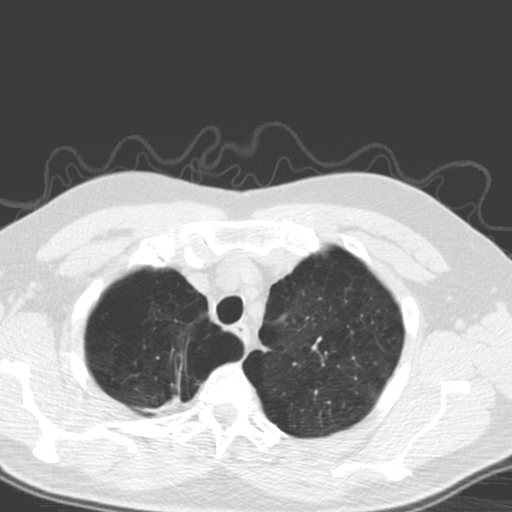
Axial slice from a low-dose chest CT screening exam. Baseline screening round. Lung window (W 1500 / L -600 HU). 3.2 mm slice thickness. 512 × 512 image matrix, field of view 340 × 340 mm. Male participant, aged 56 years at enrolment. Former smoker at enrolment.
Expert-annotated lung lesion, bounding box [x1, y1, x2, y2] px = [136, 354, 209, 423]. Screening reader's record for this exam (one nodule recorded; not confirmed to be the boxed lesion): non-calcified nodule or mass ≥4 mm, right upper lobe, 20 × 12 mm, spiculated (stellate) margins, soft tissue attenuation. Official screen result: positive, change unspecified: nodule(s) >= 4 mm or enlarging nodule(s), mass(es), or other non-specific abnormalities suspicious for lung cancer. Later outcome: lung cancer diagnosed 205 days after this screen — large cell carcinoma, NOS, right upper lobe, poorly differentiated (G3), stage IA (AJCC 6th edition), 18 mm at pathology.